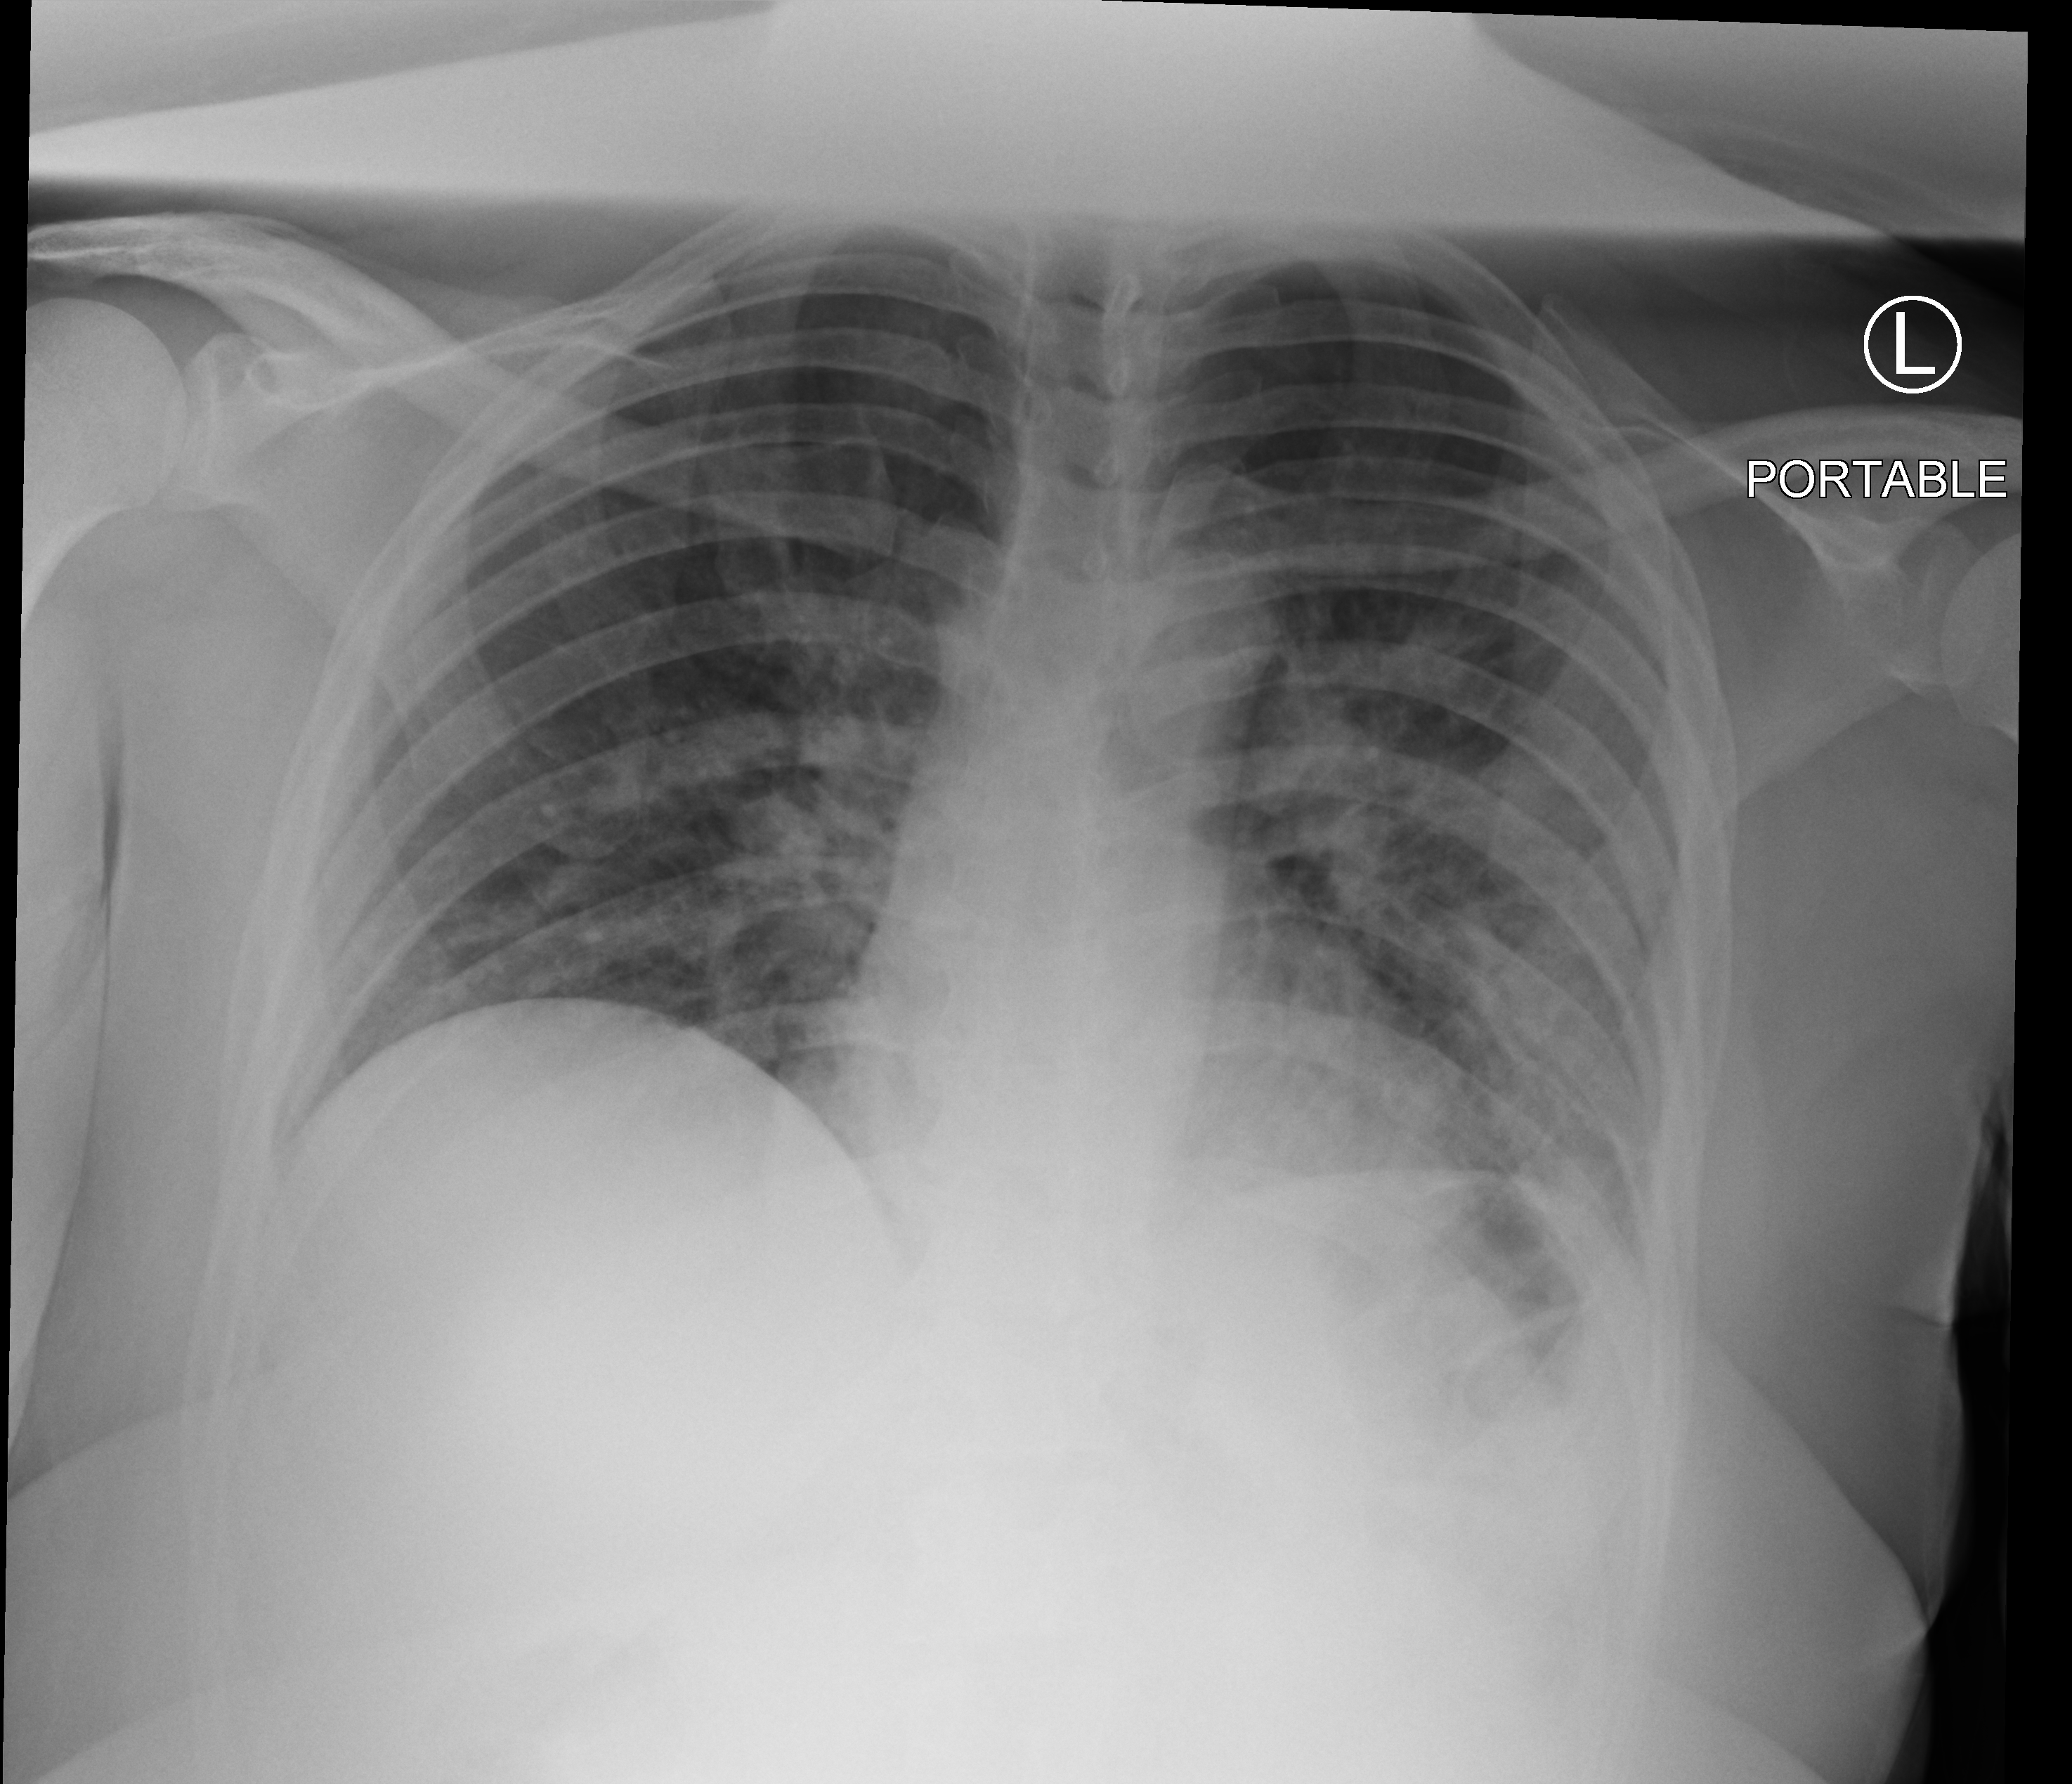
Bedside chest radiograph (computed radiography); anteroposterior (AP) projection. Patient hospitalised with COVID-19; female, aged 18–59 years.
From the hospital-stay record, not from the radiograph (when in the stay this image was taken is not recorded):
- diabetes (admission record): no